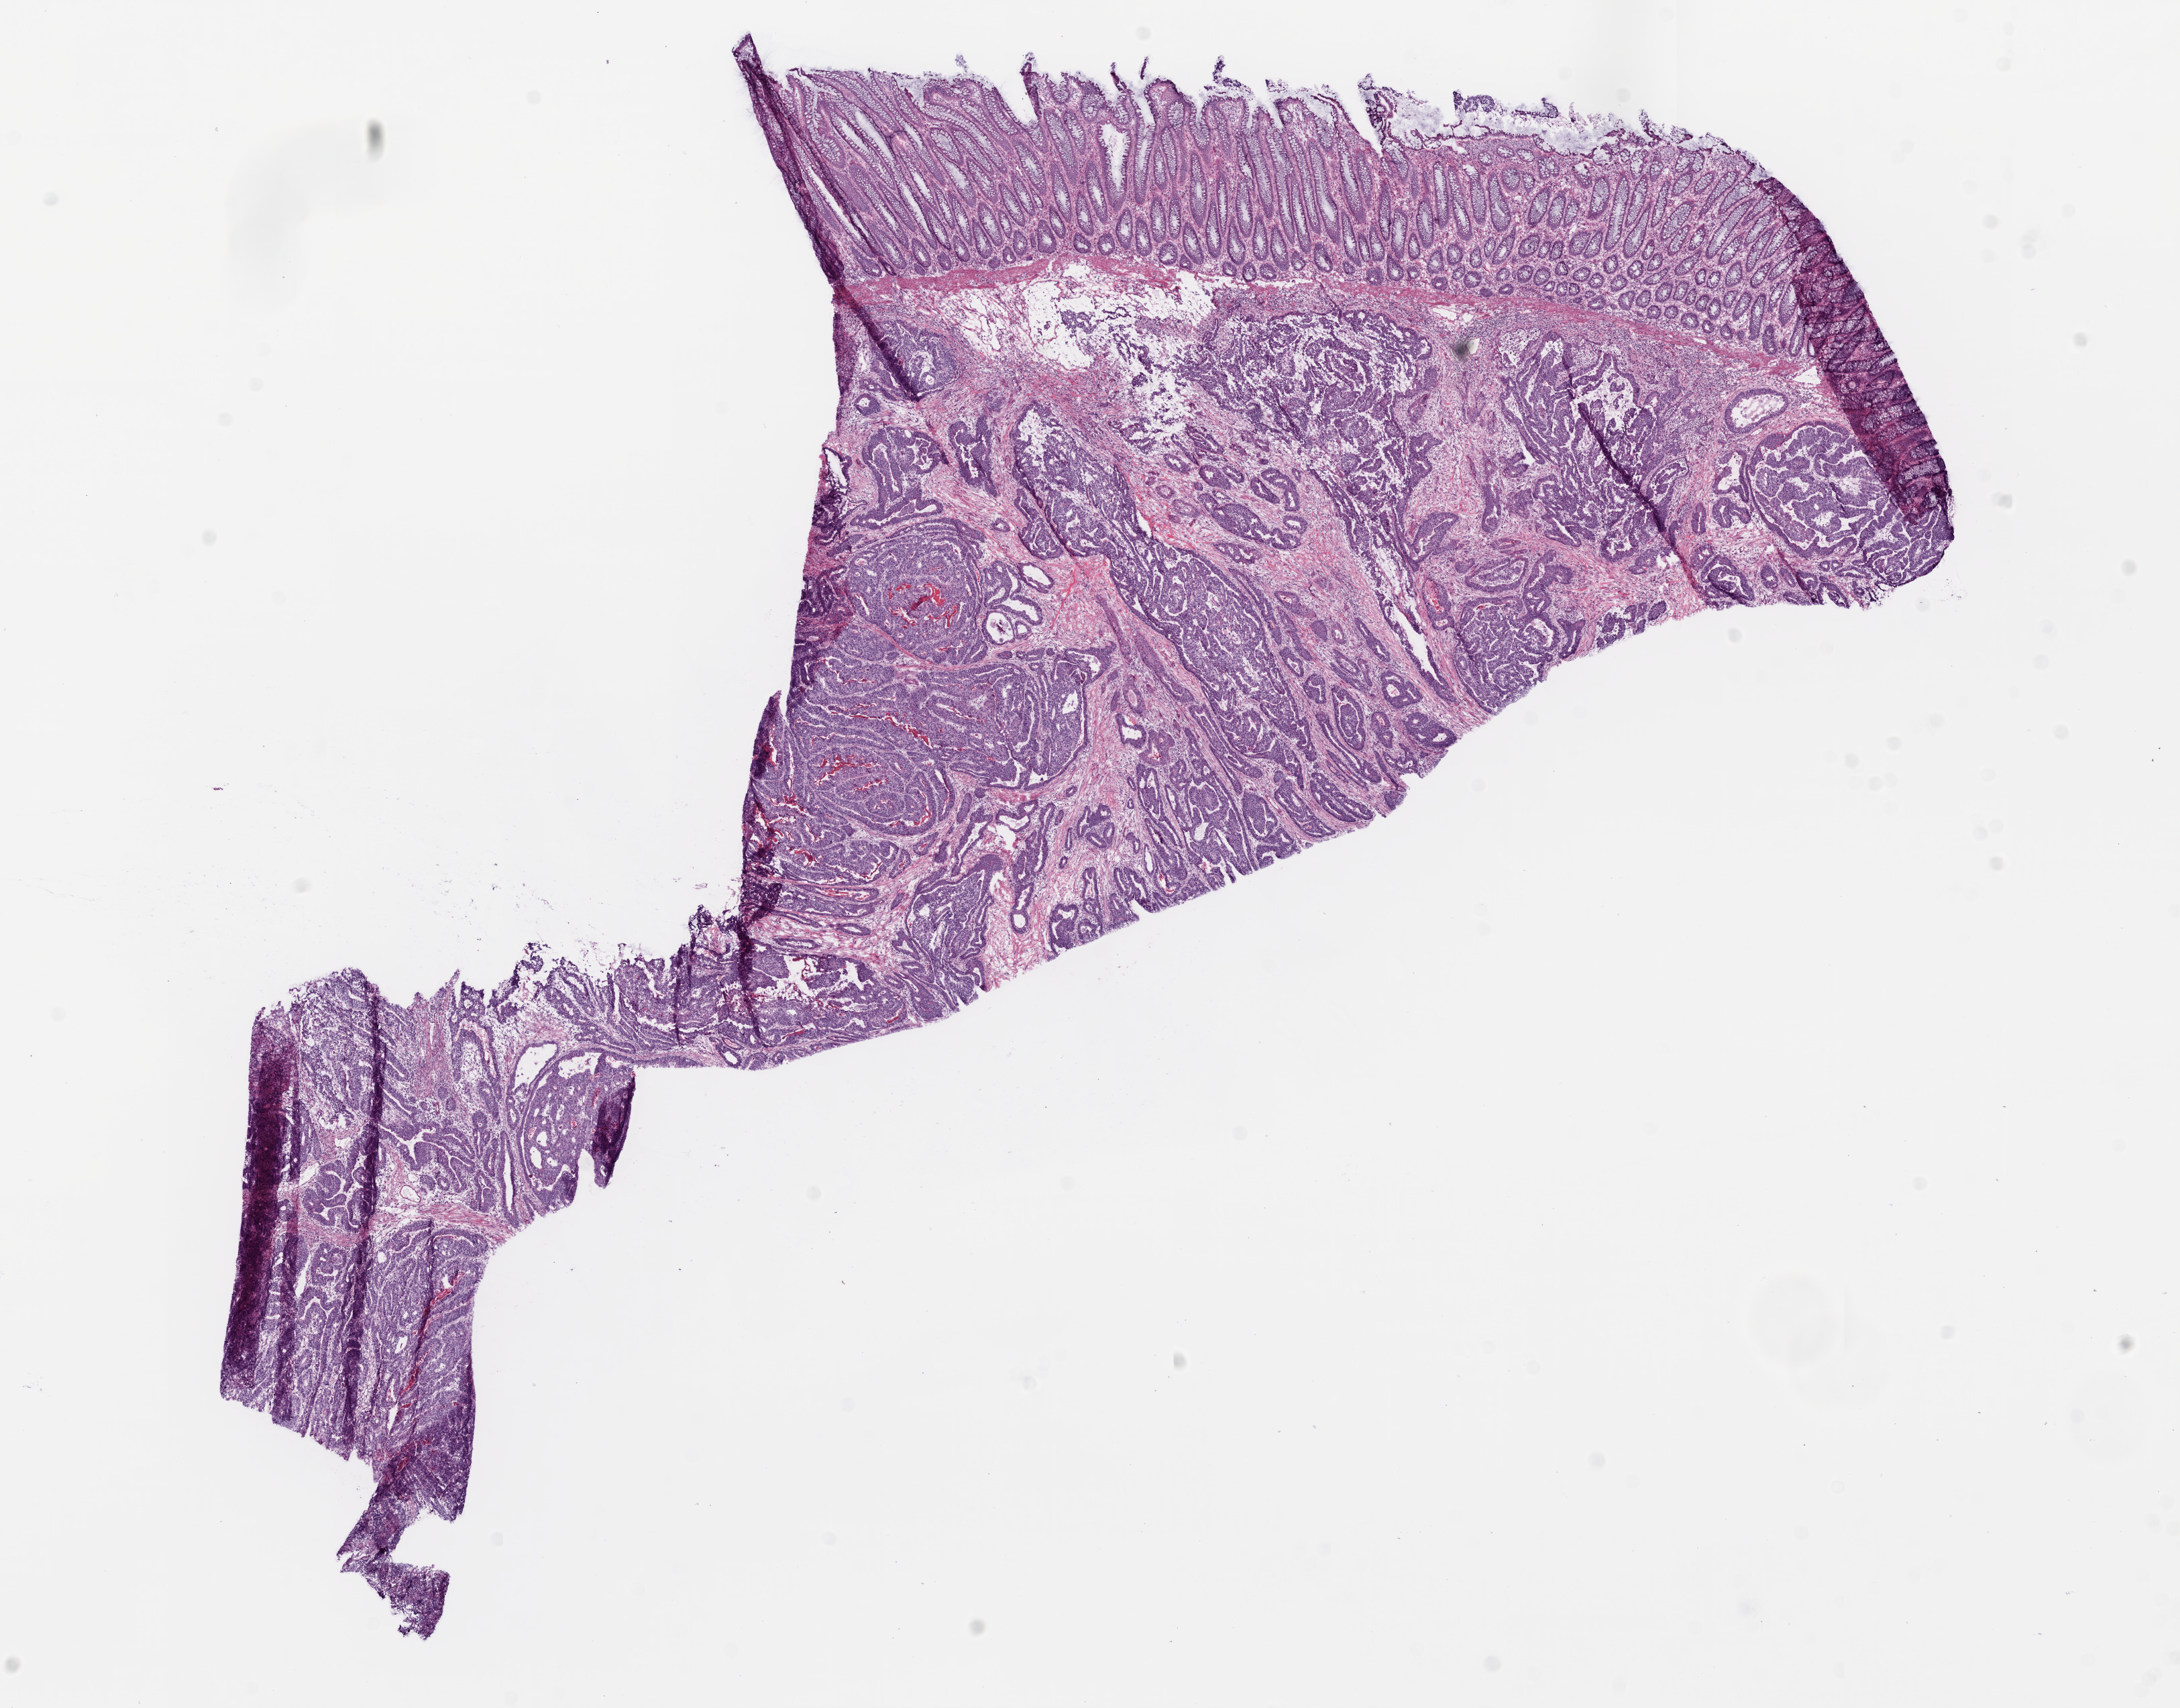
H&E whole-slide image — whole scanned area (about 13.0 x 10.2 mm, acquisition: 20x scan) shown as a low-resolution overview, frozen section, sample: primary tumour, colon. Patient: male, age at initial diagnosis 80 years. Composition of this section per pathologist review: tumour cells 60%, tumour nuclei 80%.
Diagnosis: Adenocarcinoma, NOS.